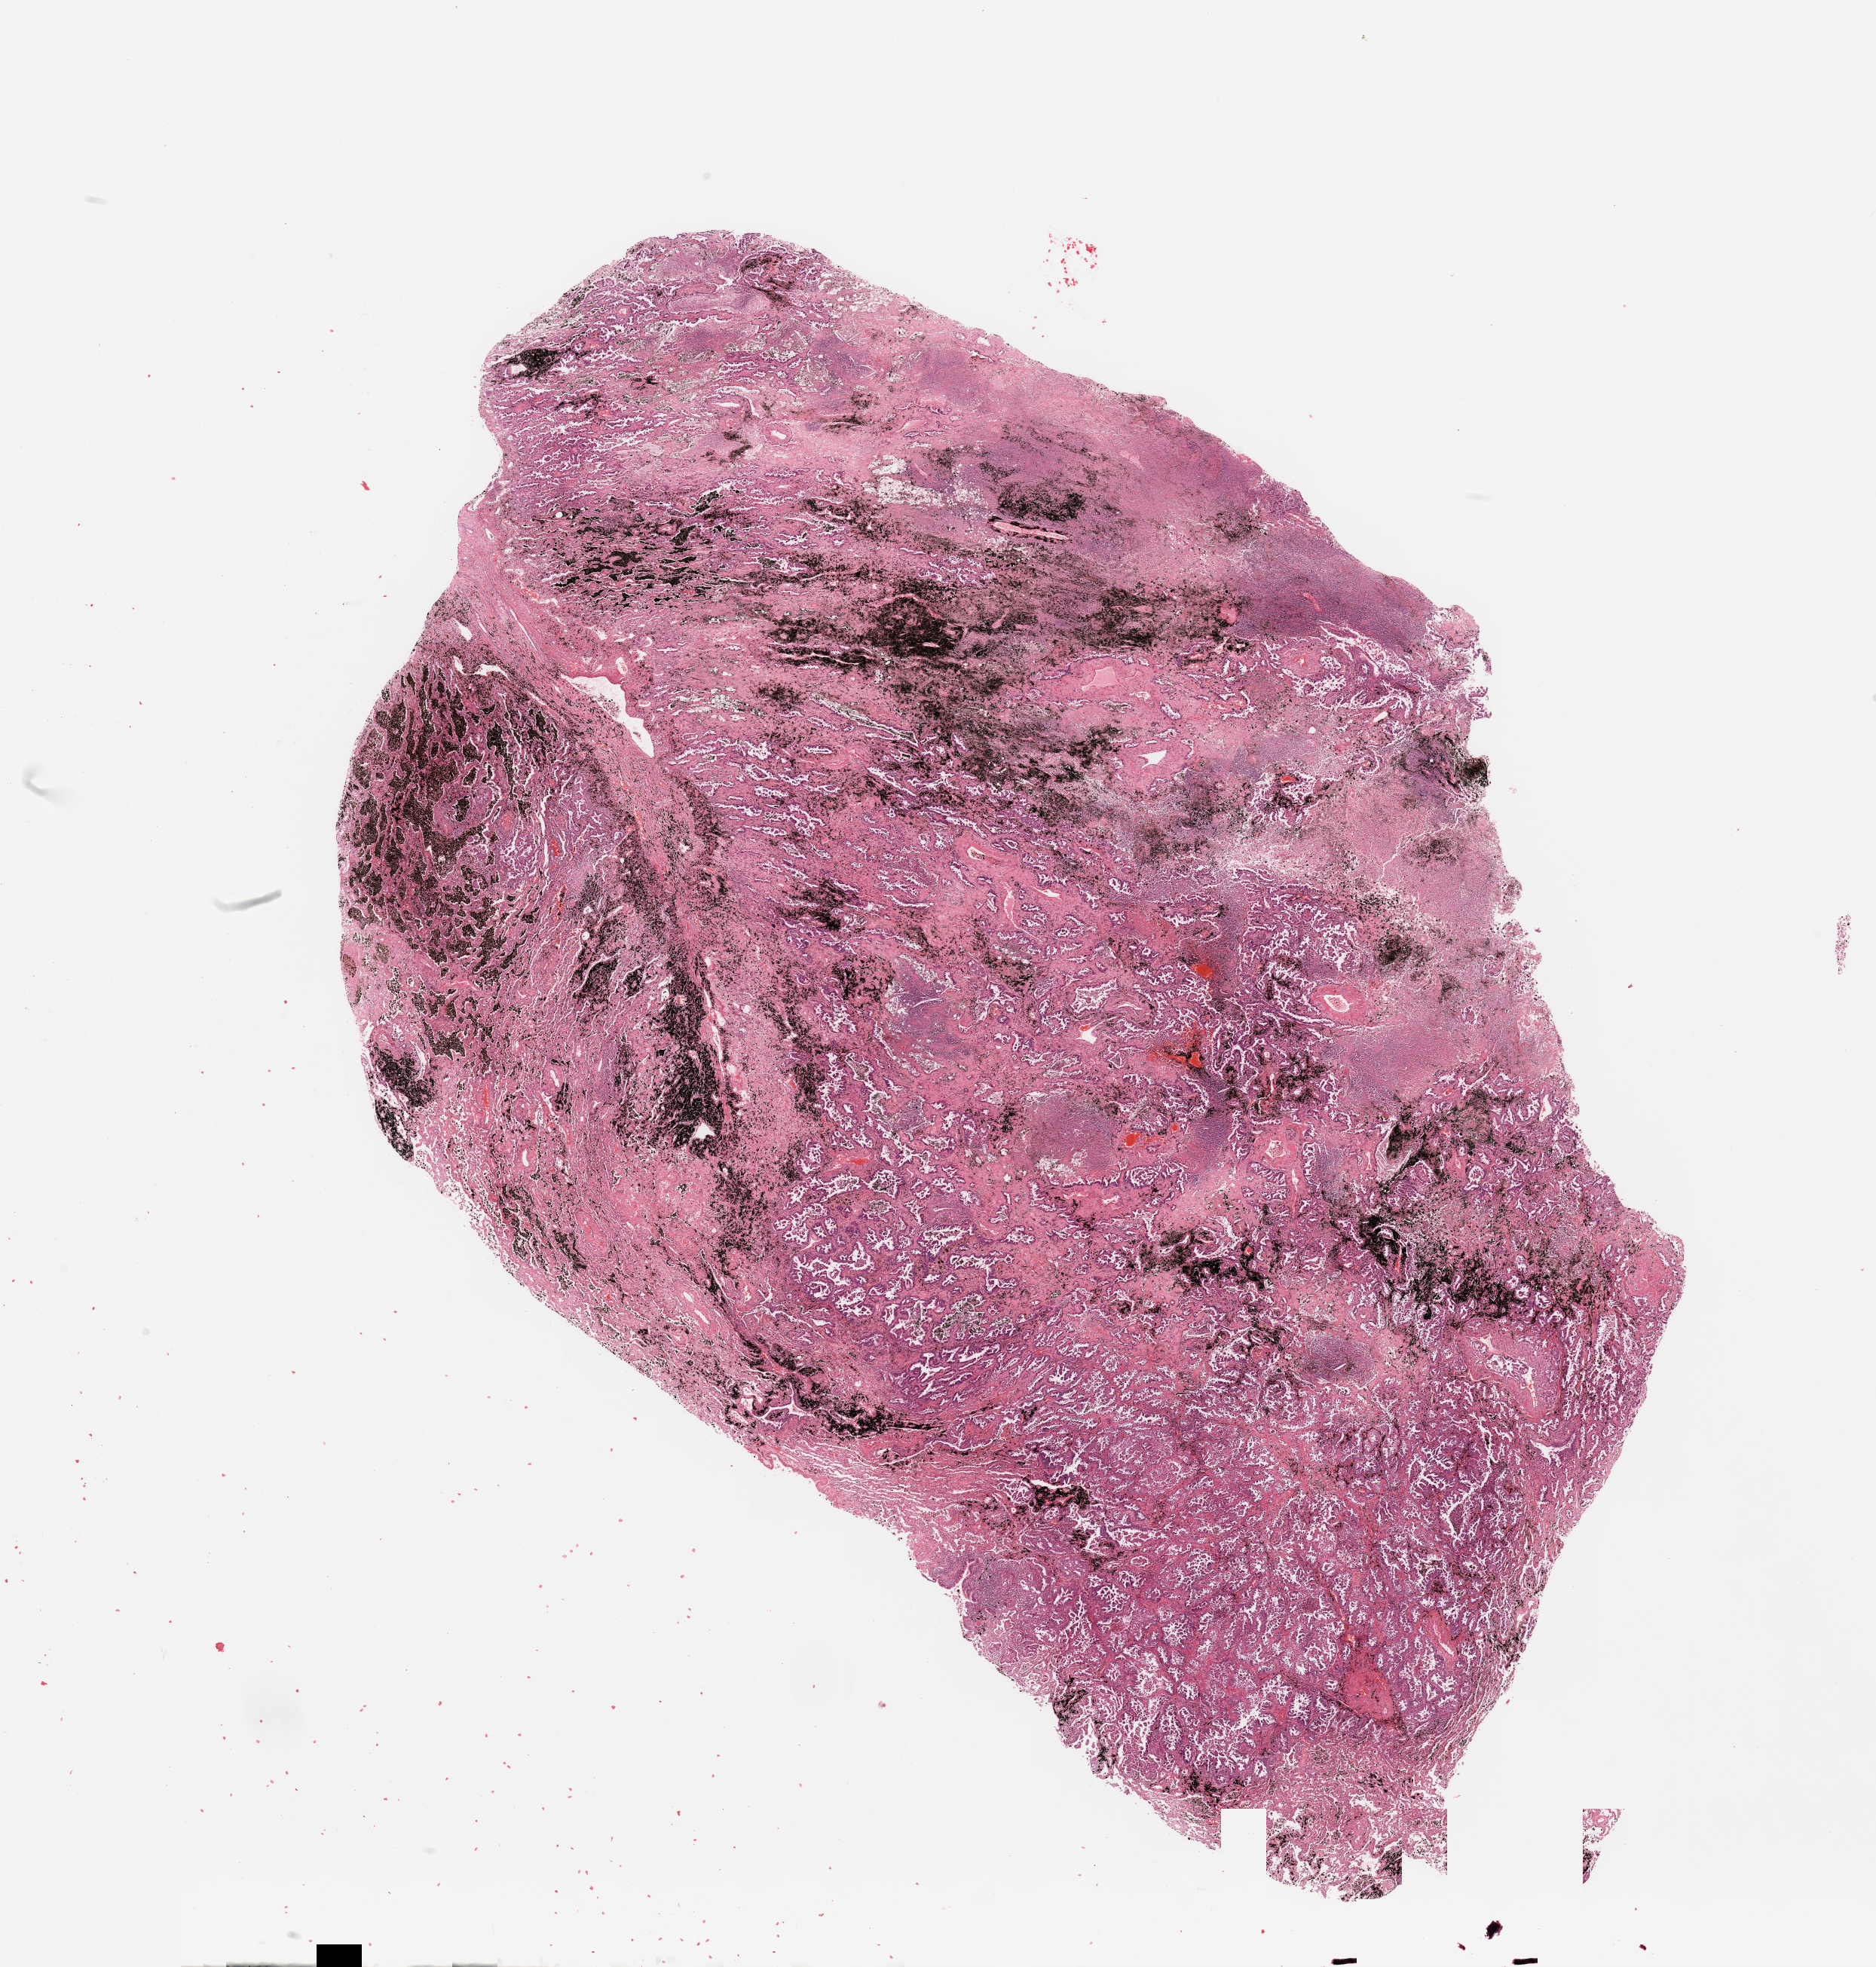
H&E-stained whole-slide image — whole scanned area (about 19.7 x 20.6 mm, acquisition: 20x scan) shown as a low-resolution overview, tumour tissue sample, lung. Male, 56 y/o. Histologic grade: G2 (moderately differentiated).
Histologic diagnosis: Adenocarcinoma, NOS. AJCC pathologic stage: IB.